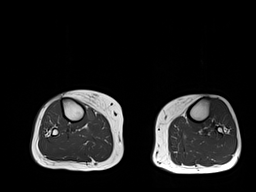
MRI of an extremity soft-tissue mass, one axial slice; 6 mm slice thickness; 256 × 192 image matrix. Female patient. From the clinical record (not read from this slice): histological type: undifferentiated – high grade; grade: high; site of the primary tumour: right thigh.
Outlined on this slice (expert manual segmentation):
- gross tumour volume (mass): bounding box (x1, y1, x2, y2) in pixels: (84, 107, 97, 122)